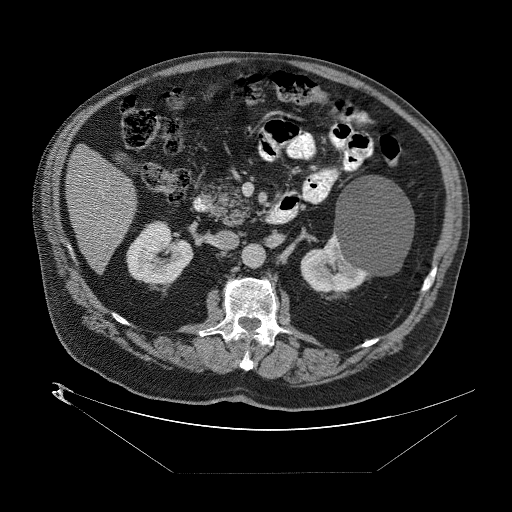
Contrast-enhanced abdominal CT (liver protocol), one axial slice. Position 21 of 89 along the scan axis. Reconstruction kernel STANDARD. 140 kVp. One of 2 acquisitions stored at this slice position. Soft-tissue window (W 400 / L 40 HU). 512 × 512 image matrix, field of view 480 × 480 mm. From the clinical record (not read from this slice): diagnosis: hepatocellular carcinoma (patient treated with transarterial chemoembolisation; whether this scan precedes or follows treatment is not stated here); TNM stage (as recorded): Stage-II.
Outlined on this slice (semi-automatic segmentation, software-assisted and operator-edited):
- abdominal aorta: bounding box (x1, y1, x2, y2) in pixels: (244, 244, 265, 266)
- liver parenchyma outside the tumour (the mass and vessels are separate outlines, so this box may not span the whole liver): (64, 141, 136, 269)
- liver vessels: (91, 169, 104, 237)